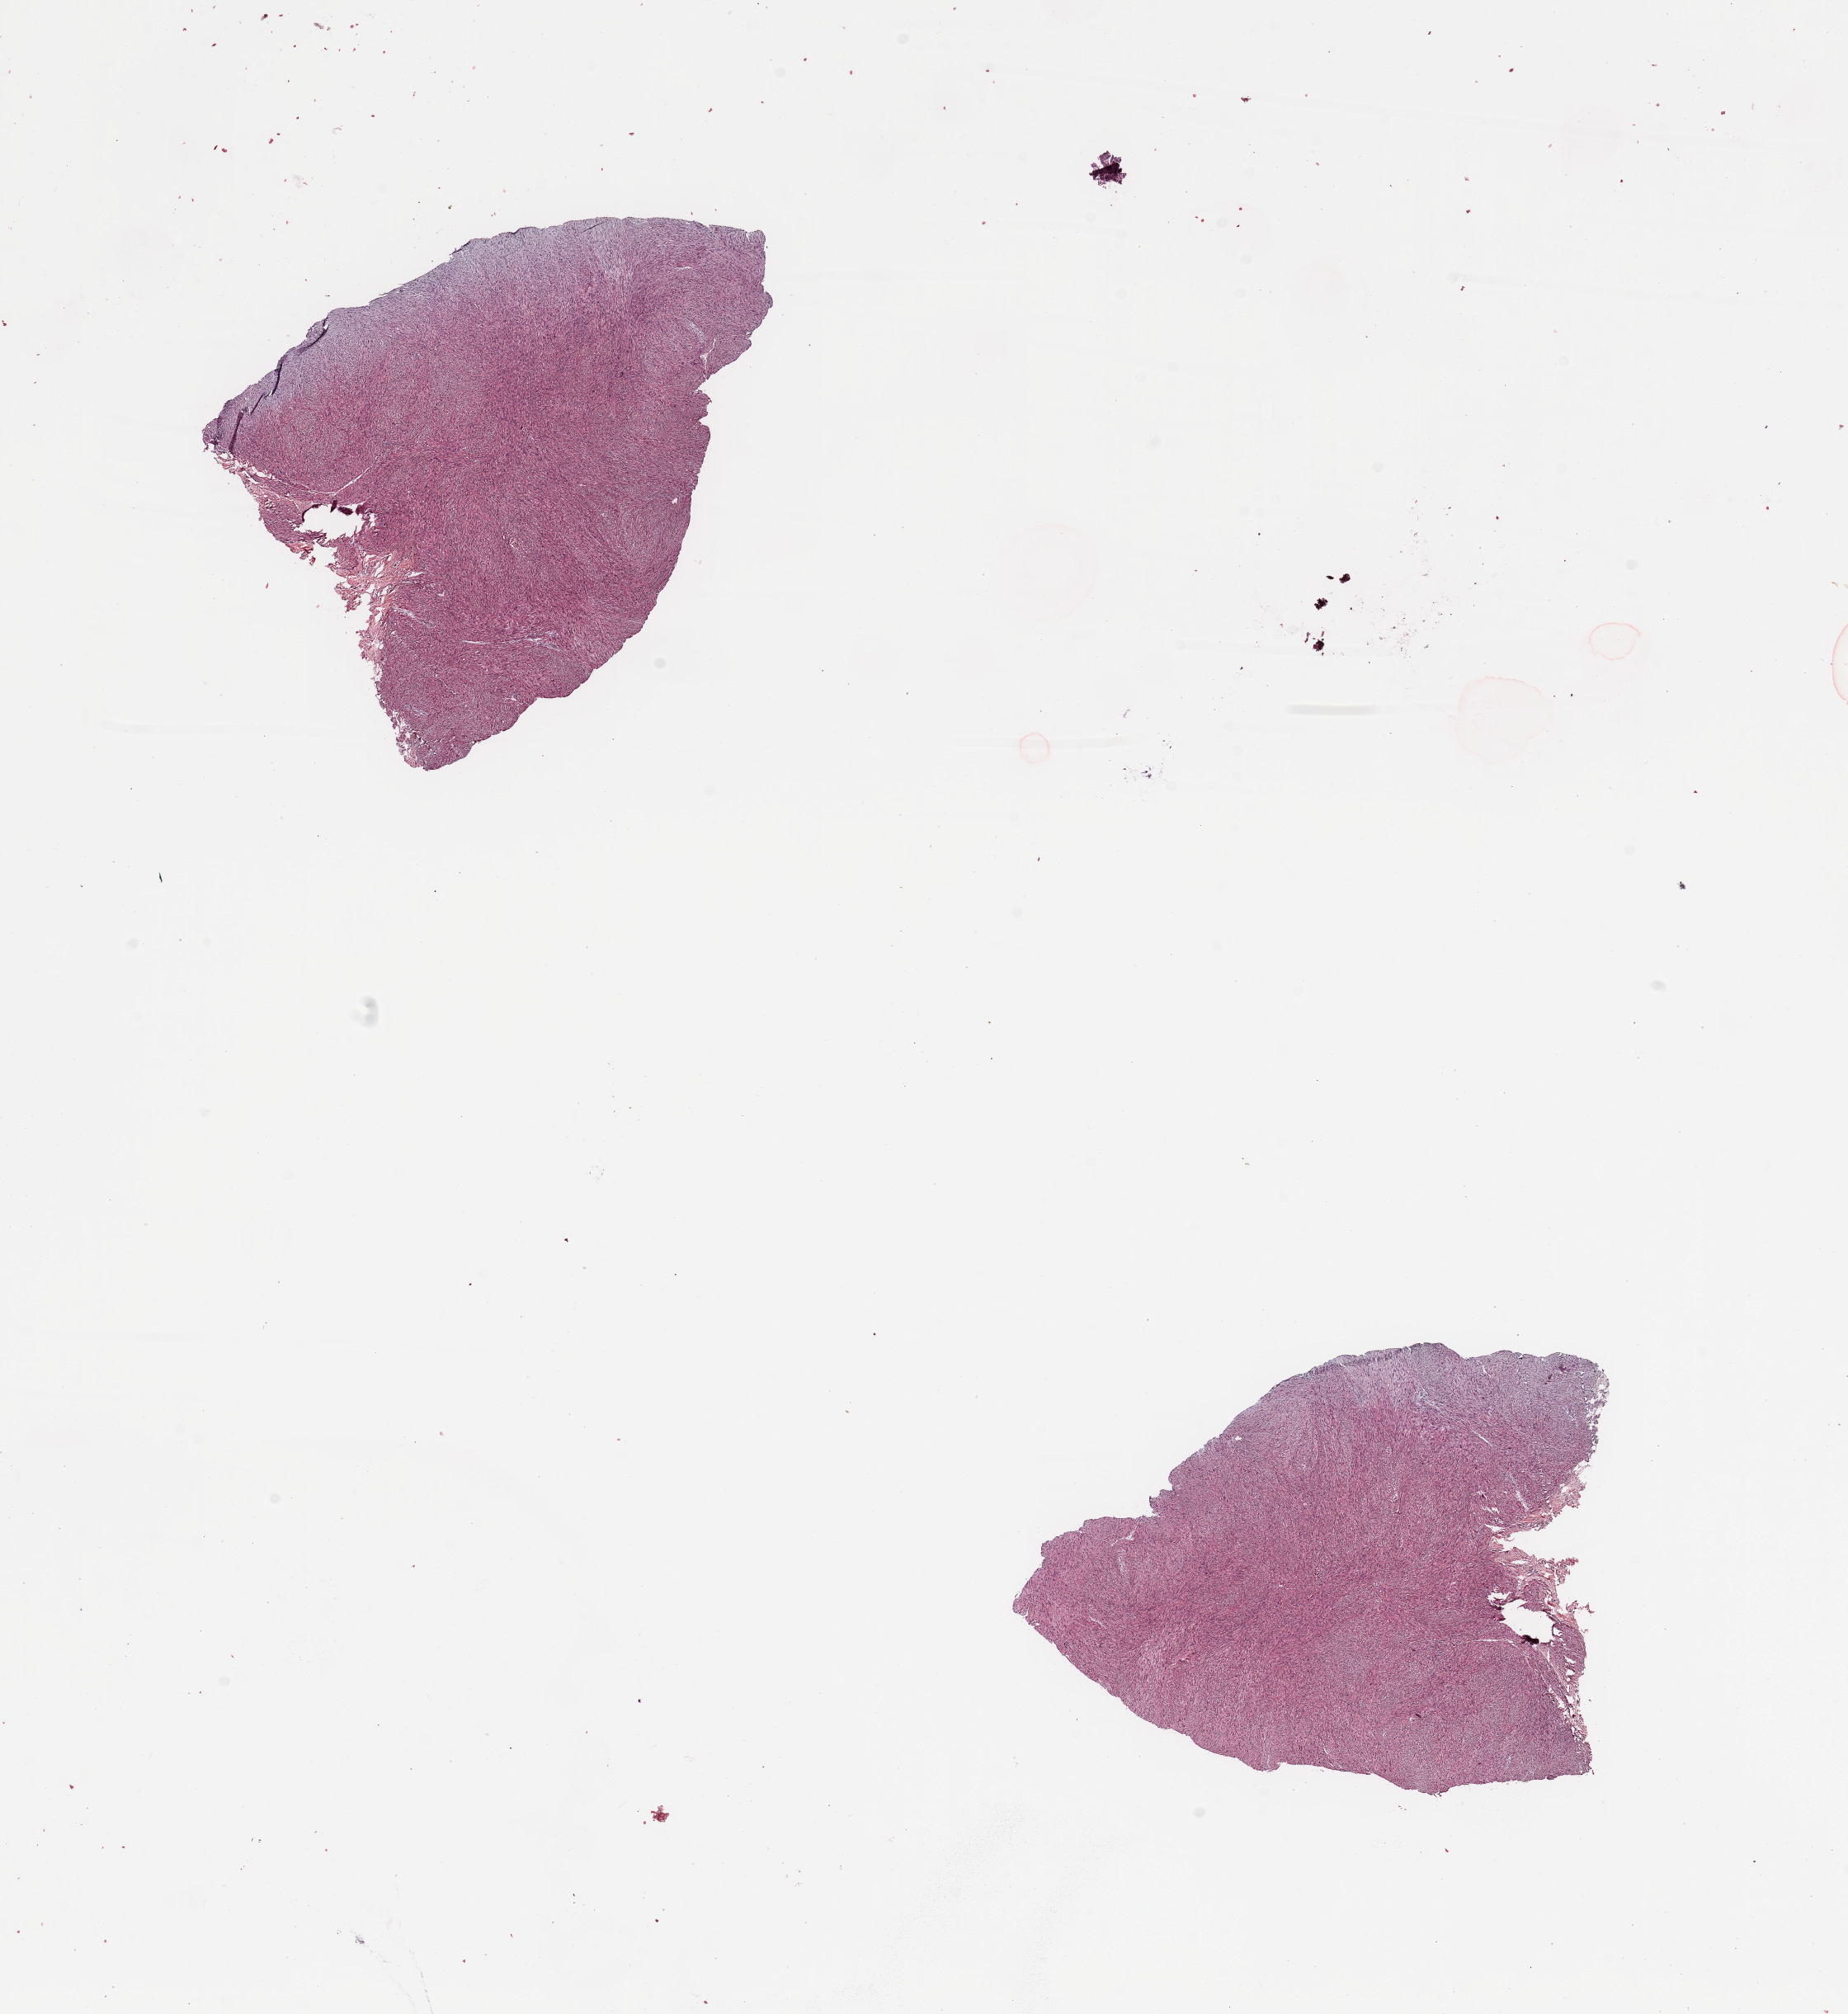
Digitized H&E-stained tissue section (whole slide) — shown as a low-resolution overview of the whole scanned area (about 17.7 x 19.3 mm). Tumour tissue sample. 76-year-old female patient.
Primary tumour site (as recorded): superficial trunk. Patient diagnosis (cohort enrolment): sarcoma (site not recorded at cohort level).